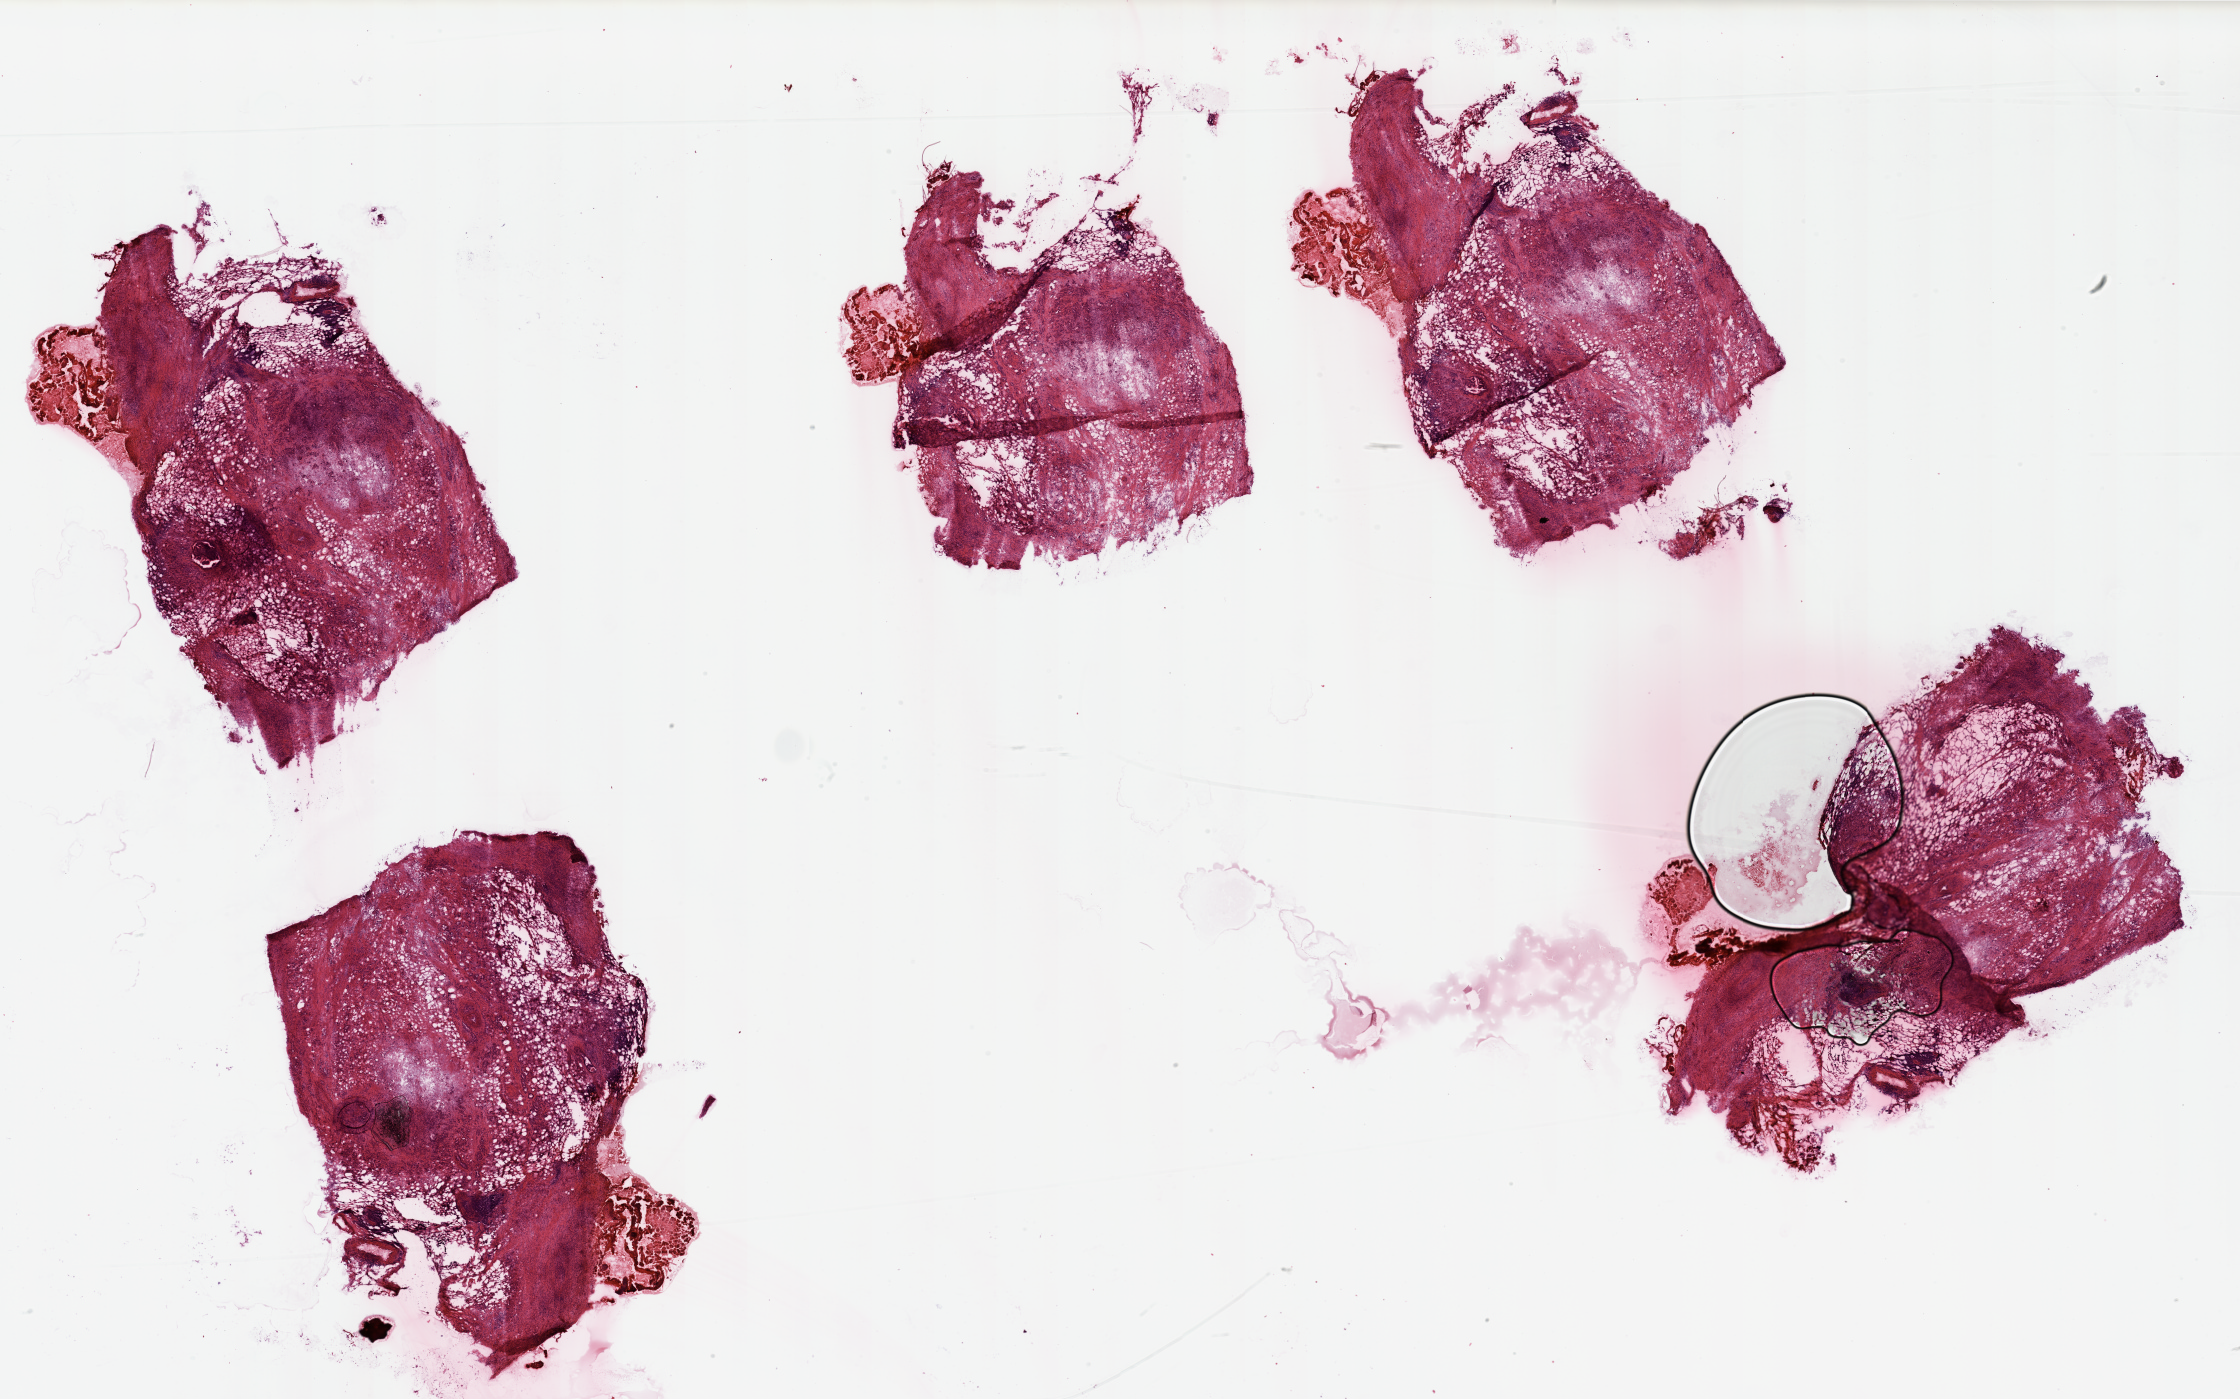
Digitized H&E tissue section (whole slide), low-resolution overview of the scanned area, about 35.4 x 22.1 mm; tumour tissue sample, pancreas. Male, 65 y/o. Histologic grade: G3 (poorly differentiated).
Diagnosis: Infiltrating duct carcinoma, NOS. AJCC pathologic stage: III. Primary tumour site (as recorded): head.